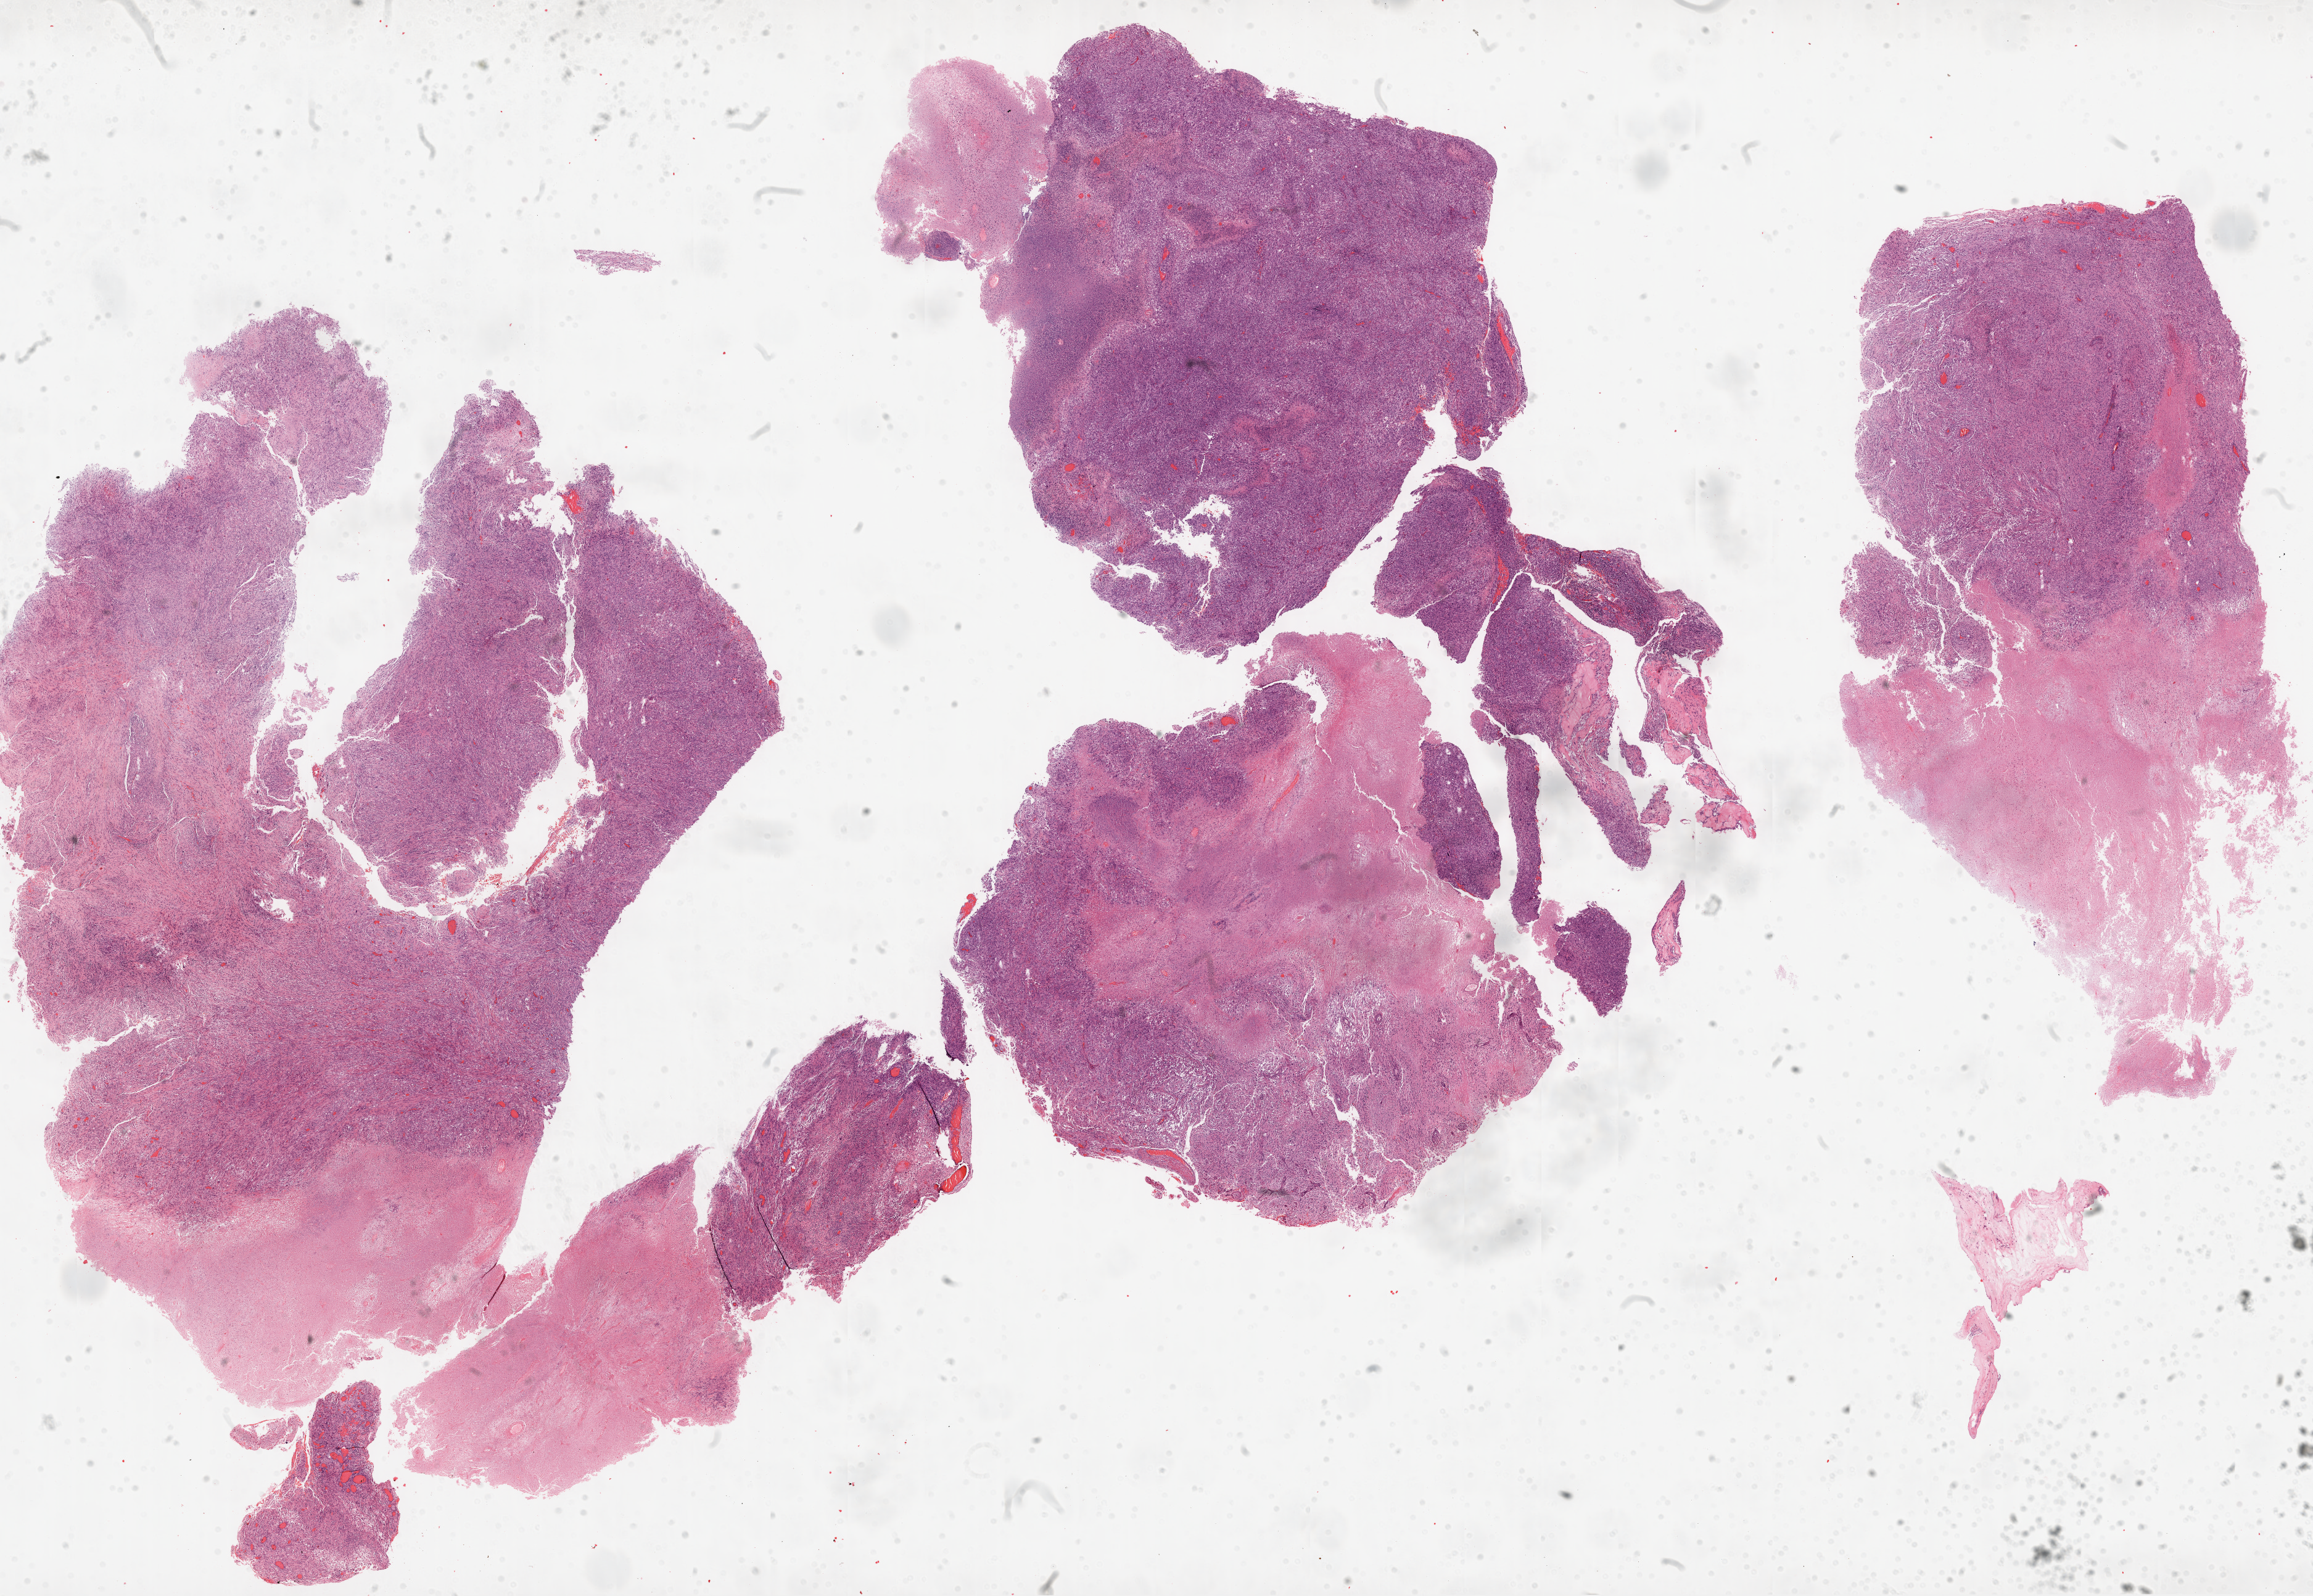
Whole-slide histology image, H&E-stained, whole scanned area (about 30.1 x 20.8 mm, acquisition: 20x scan) shown as a low-resolution overview, formalin-fixed paraffin-embedded (FFPE) diagnostic section, primary tumour sample from the brain. Male patient; age at initial diagnosis 54 years.
* pathologic diagnosis: Glioblastoma